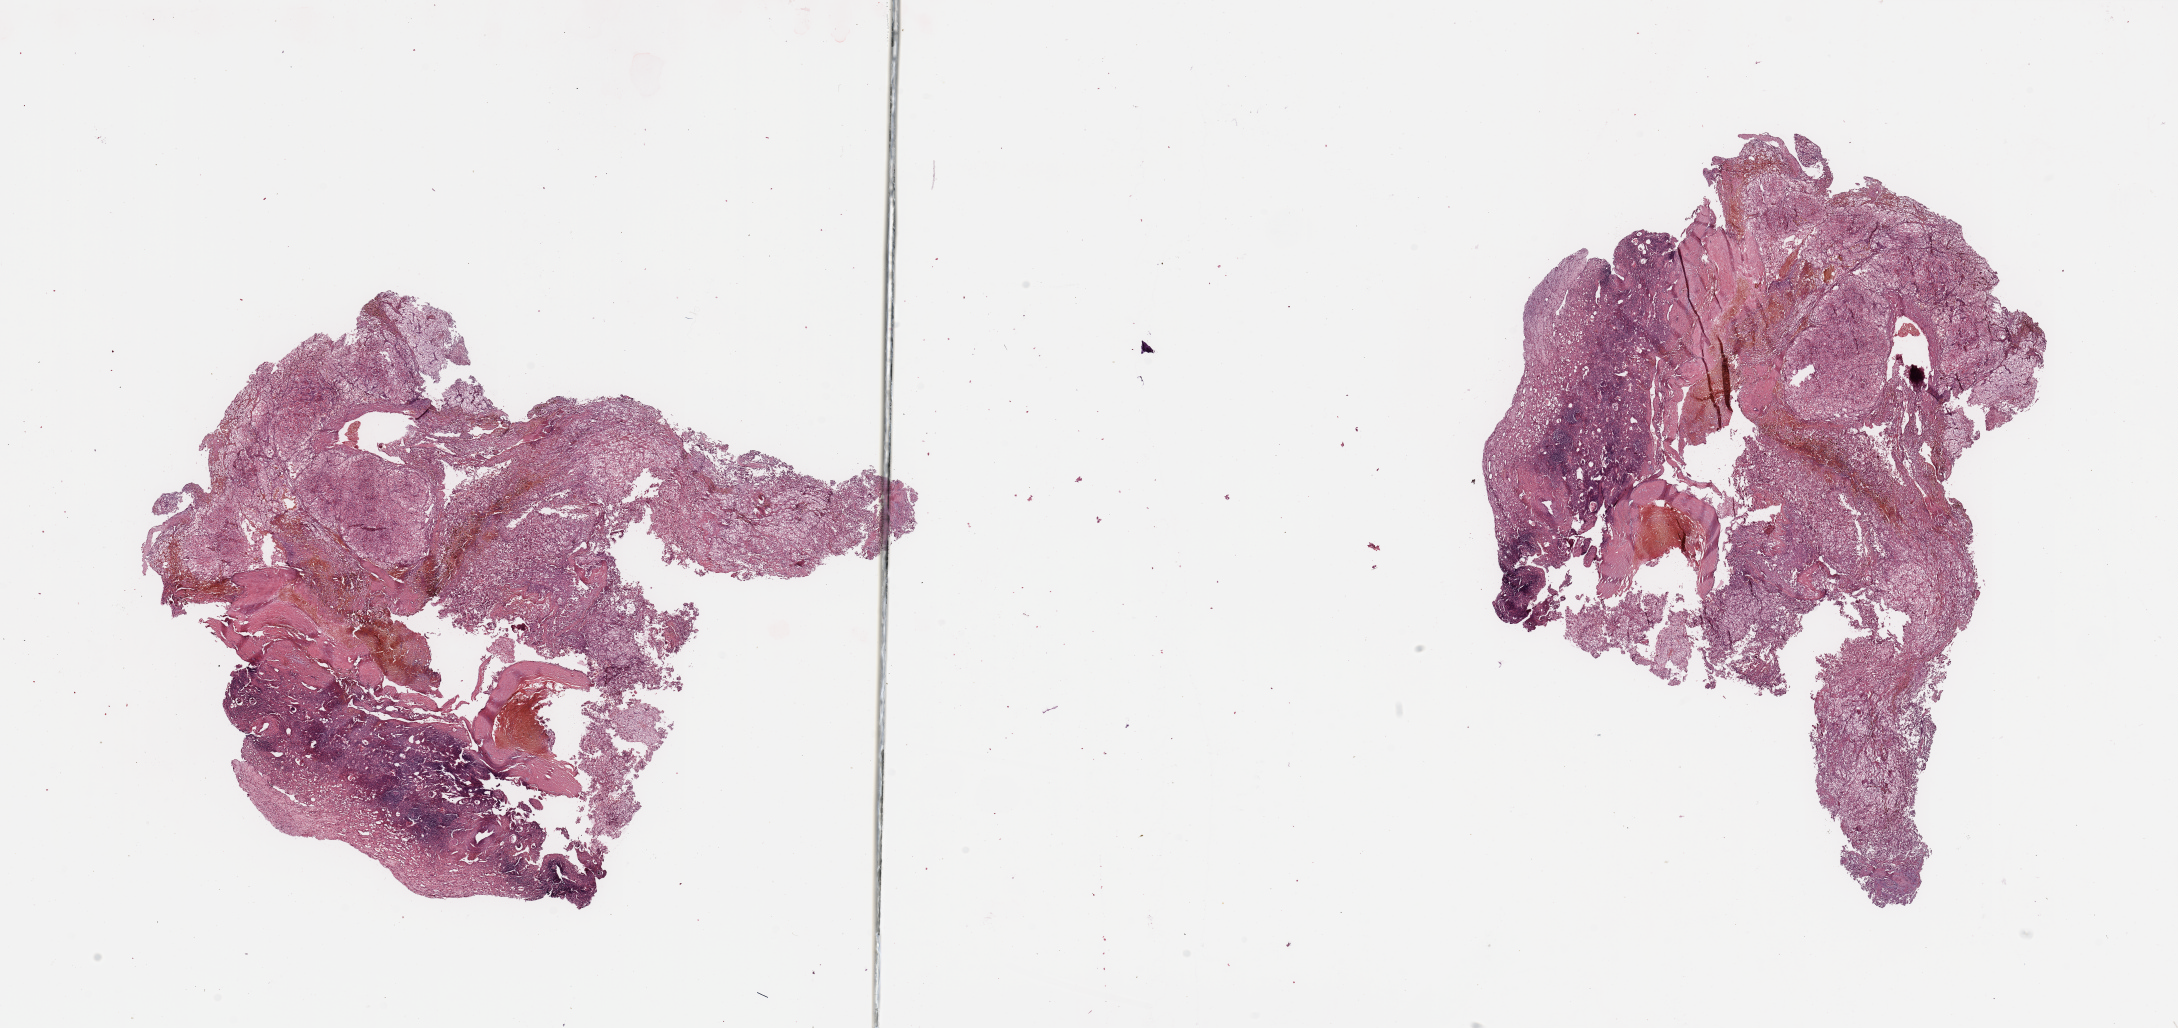
H&E whole-slide image, a low-resolution overview of the entire scanned area, about 34.5 x 16.3 mm (slide scanned at 20x). Kidney, tumour tissue. 58-year-old male patient. Histologic grade: G2 (moderately differentiated).
AJCC pathologic stage: III. Diagnosis: Renal cell carcinoma, NOS.